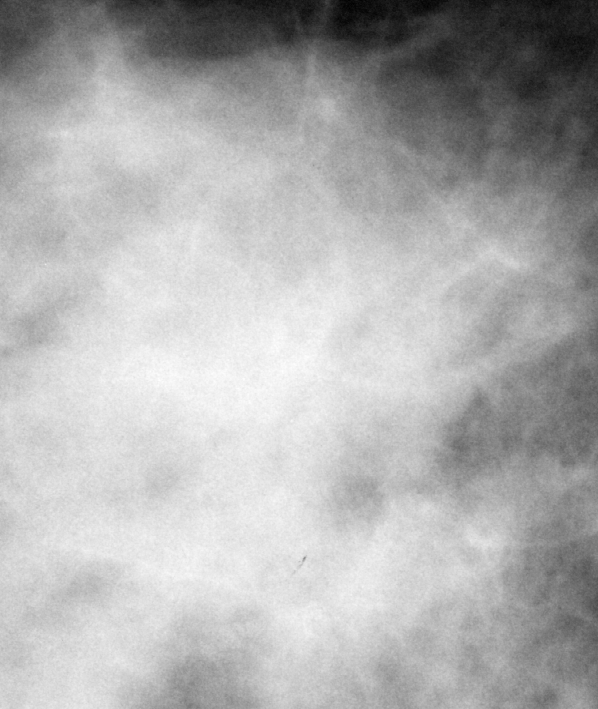
Cropped region of a digitized screen-film mammogram centred on a radiologist-marked abnormality, right breast, MLO view, BI-RADS breast density category 2 (scale 1–4).
Marked abnormality: mass, shape asymmetric breast tissue, margins ill defined; BI-RADS assessment category 5; pathology result (as recorded, not read from the image): malignant.